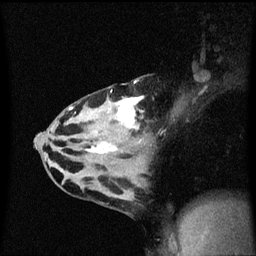
Breast MRI (dynamic contrast-enhanced), one sagittal slice; slice 31 of 60 in the series (ordered by position); dynamic contrast-enhanced series, image 2 of 3 at this slice position (ordered by acquisition); 1.5 T; TE 4.2 ms, TR 8.4 ms; 256 × 256 image matrix. Female patient, age 32 years.
Structures marked on this image (semi-automatically segmented with operator editing):
- analysis volume of interest (the breast-tissue region the enhancement analysis was run in; not a lesion): bounding box [x1, y1, x2, y2] px = [55, 78, 179, 167]
- tumour enhancement mask (voxels above the 70 % enhancement threshold inside the analysis volume of interest): [86, 80, 145, 155]